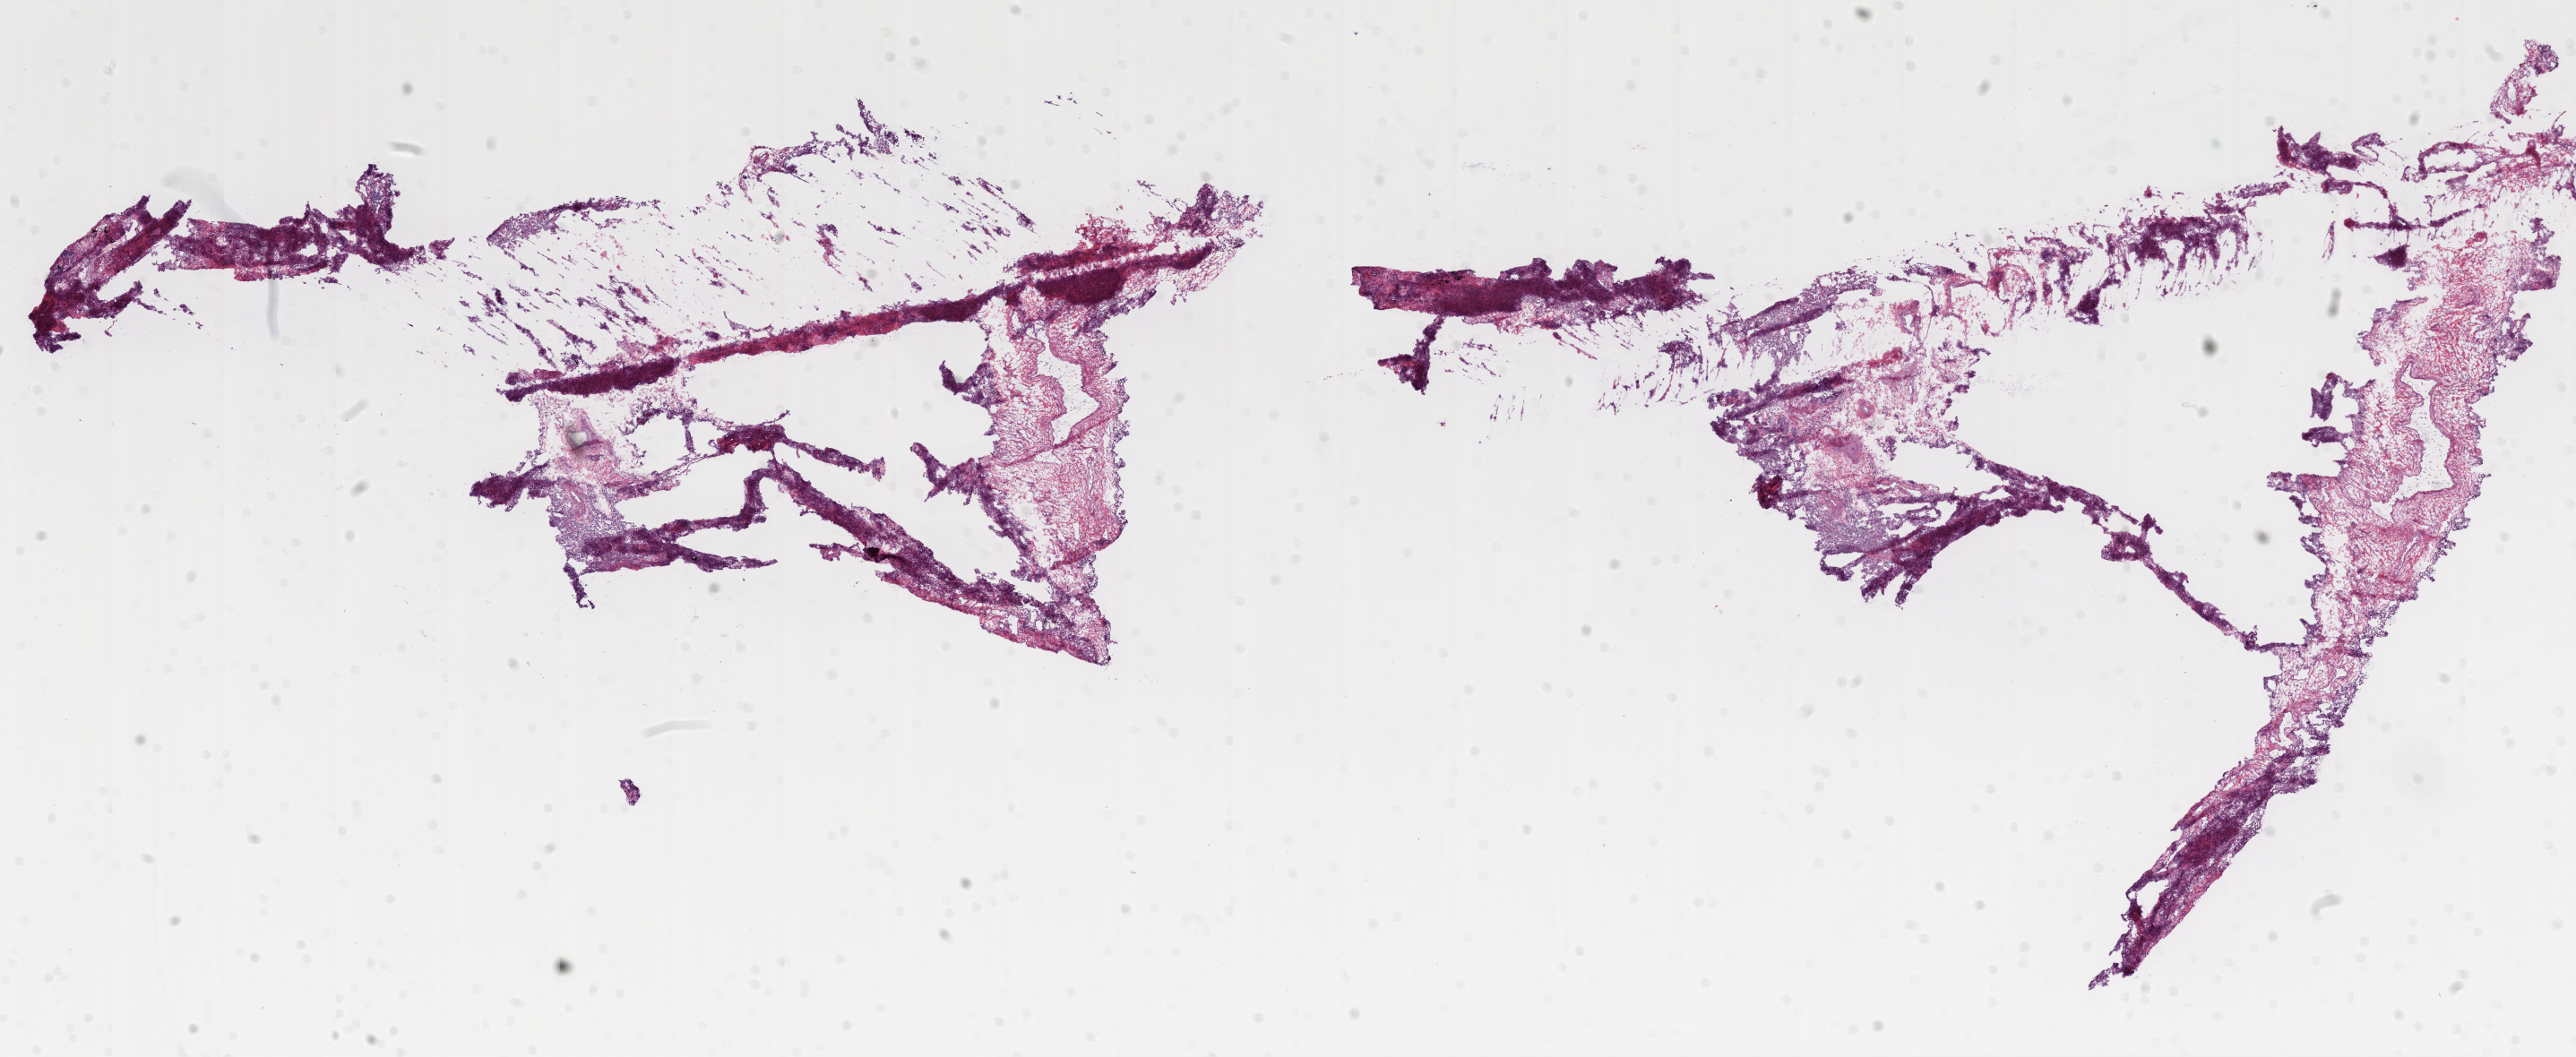
Whole-slide histology image, H&E — low-resolution overview of the scanned area, about 23.1 x 9.5 mm (slide scanned at 20x); frozen section; sample: solid tissue normal (non-tumour tissue), lung. Male patient; age at initial diagnosis 66 years.
This section: solid tissue normal sample (biorepository sample class). Patient diagnosis: Squamous cell carcinoma, NOS (lower lobe, lung).